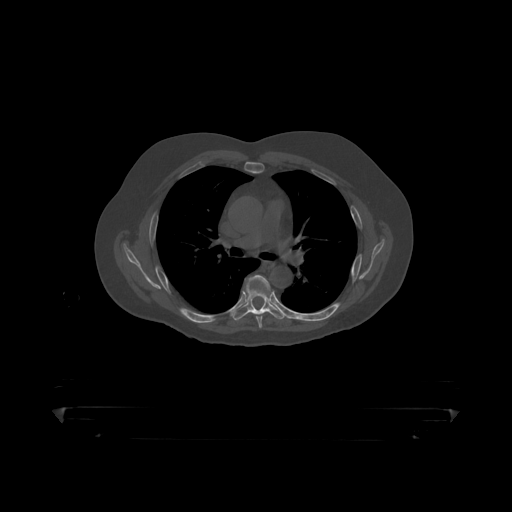
CT including the spine, one axial slice; position 308 of 390 along the scan axis; reconstruction kernel STANDARD; 120 kVp; bone window (W 1800 / L 400 HU); 1.25 mm slice thickness; 512 × 512 image matrix, field of view 650 × 650 mm. Patient: male, 60 years. Case-level facts recorded for this patient, not image findings: primary cancer: prostate.
Outlined on this slice (semi-automatically segmented with operator editing):
- T5 vertebra: bounding box [x1, y1, x2, y2] px = [246, 275, 270, 319]
- T6 vertebra: [234, 281, 283, 318]